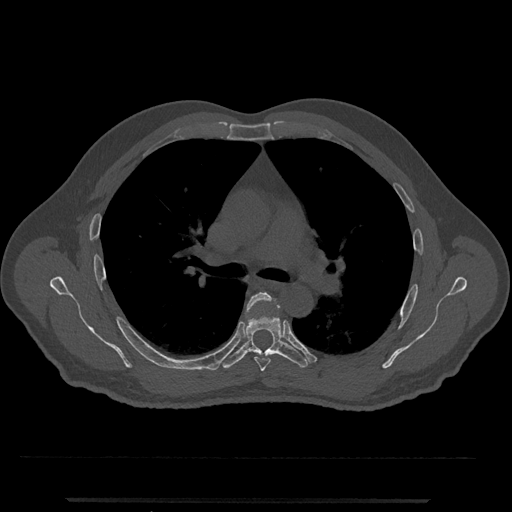
CT including the spine, one axial slice; slice 761 of 797 in the series (ordered by position); reconstruction kernel Br40s/3; 120 kVp; bone window (W 1800 / L 400 HU); 0.5 mm slice thickness; 512 × 512 image matrix, field of view 419 × 419 mm. Patient: male, 63 years. From the clinical record (not read from this slice): primary cancer: prostate.
Structures marked on this image (semi-automatic segmentation, software-assisted and operator-edited):
- T5 vertebra: bounding box <245,292,276,372> (left, top, right, bottom; pixels)
- T6 vertebra: <221,297,310,369>